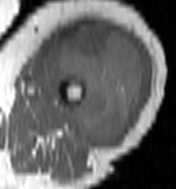
MRI of an extremity soft-tissue mass, one axial slice; position 56 of 100 along the scan axis; MR volume resampled by the dataset authors to the PET/CT grid (not the native acquisition matrix); 3.27 mm slice thickness; 176 × 189 image matrix, field of view 172 × 185 mm. Female patient. From the clinical record (not read from this slice): histological type: undifferentiated – high grade; grade: high; site of the primary tumour: left thigh.
Annotated regions visible in this slice (expert contour drawn on MRI and transferred to this co-registered scan by the dataset authors):
- gross tumour volume including surrounding oedema: bounding box (x1, y1, x2, y2) in pixels: (46, 25, 145, 149)
- gross tumour volume (mass): (46, 25, 145, 149)